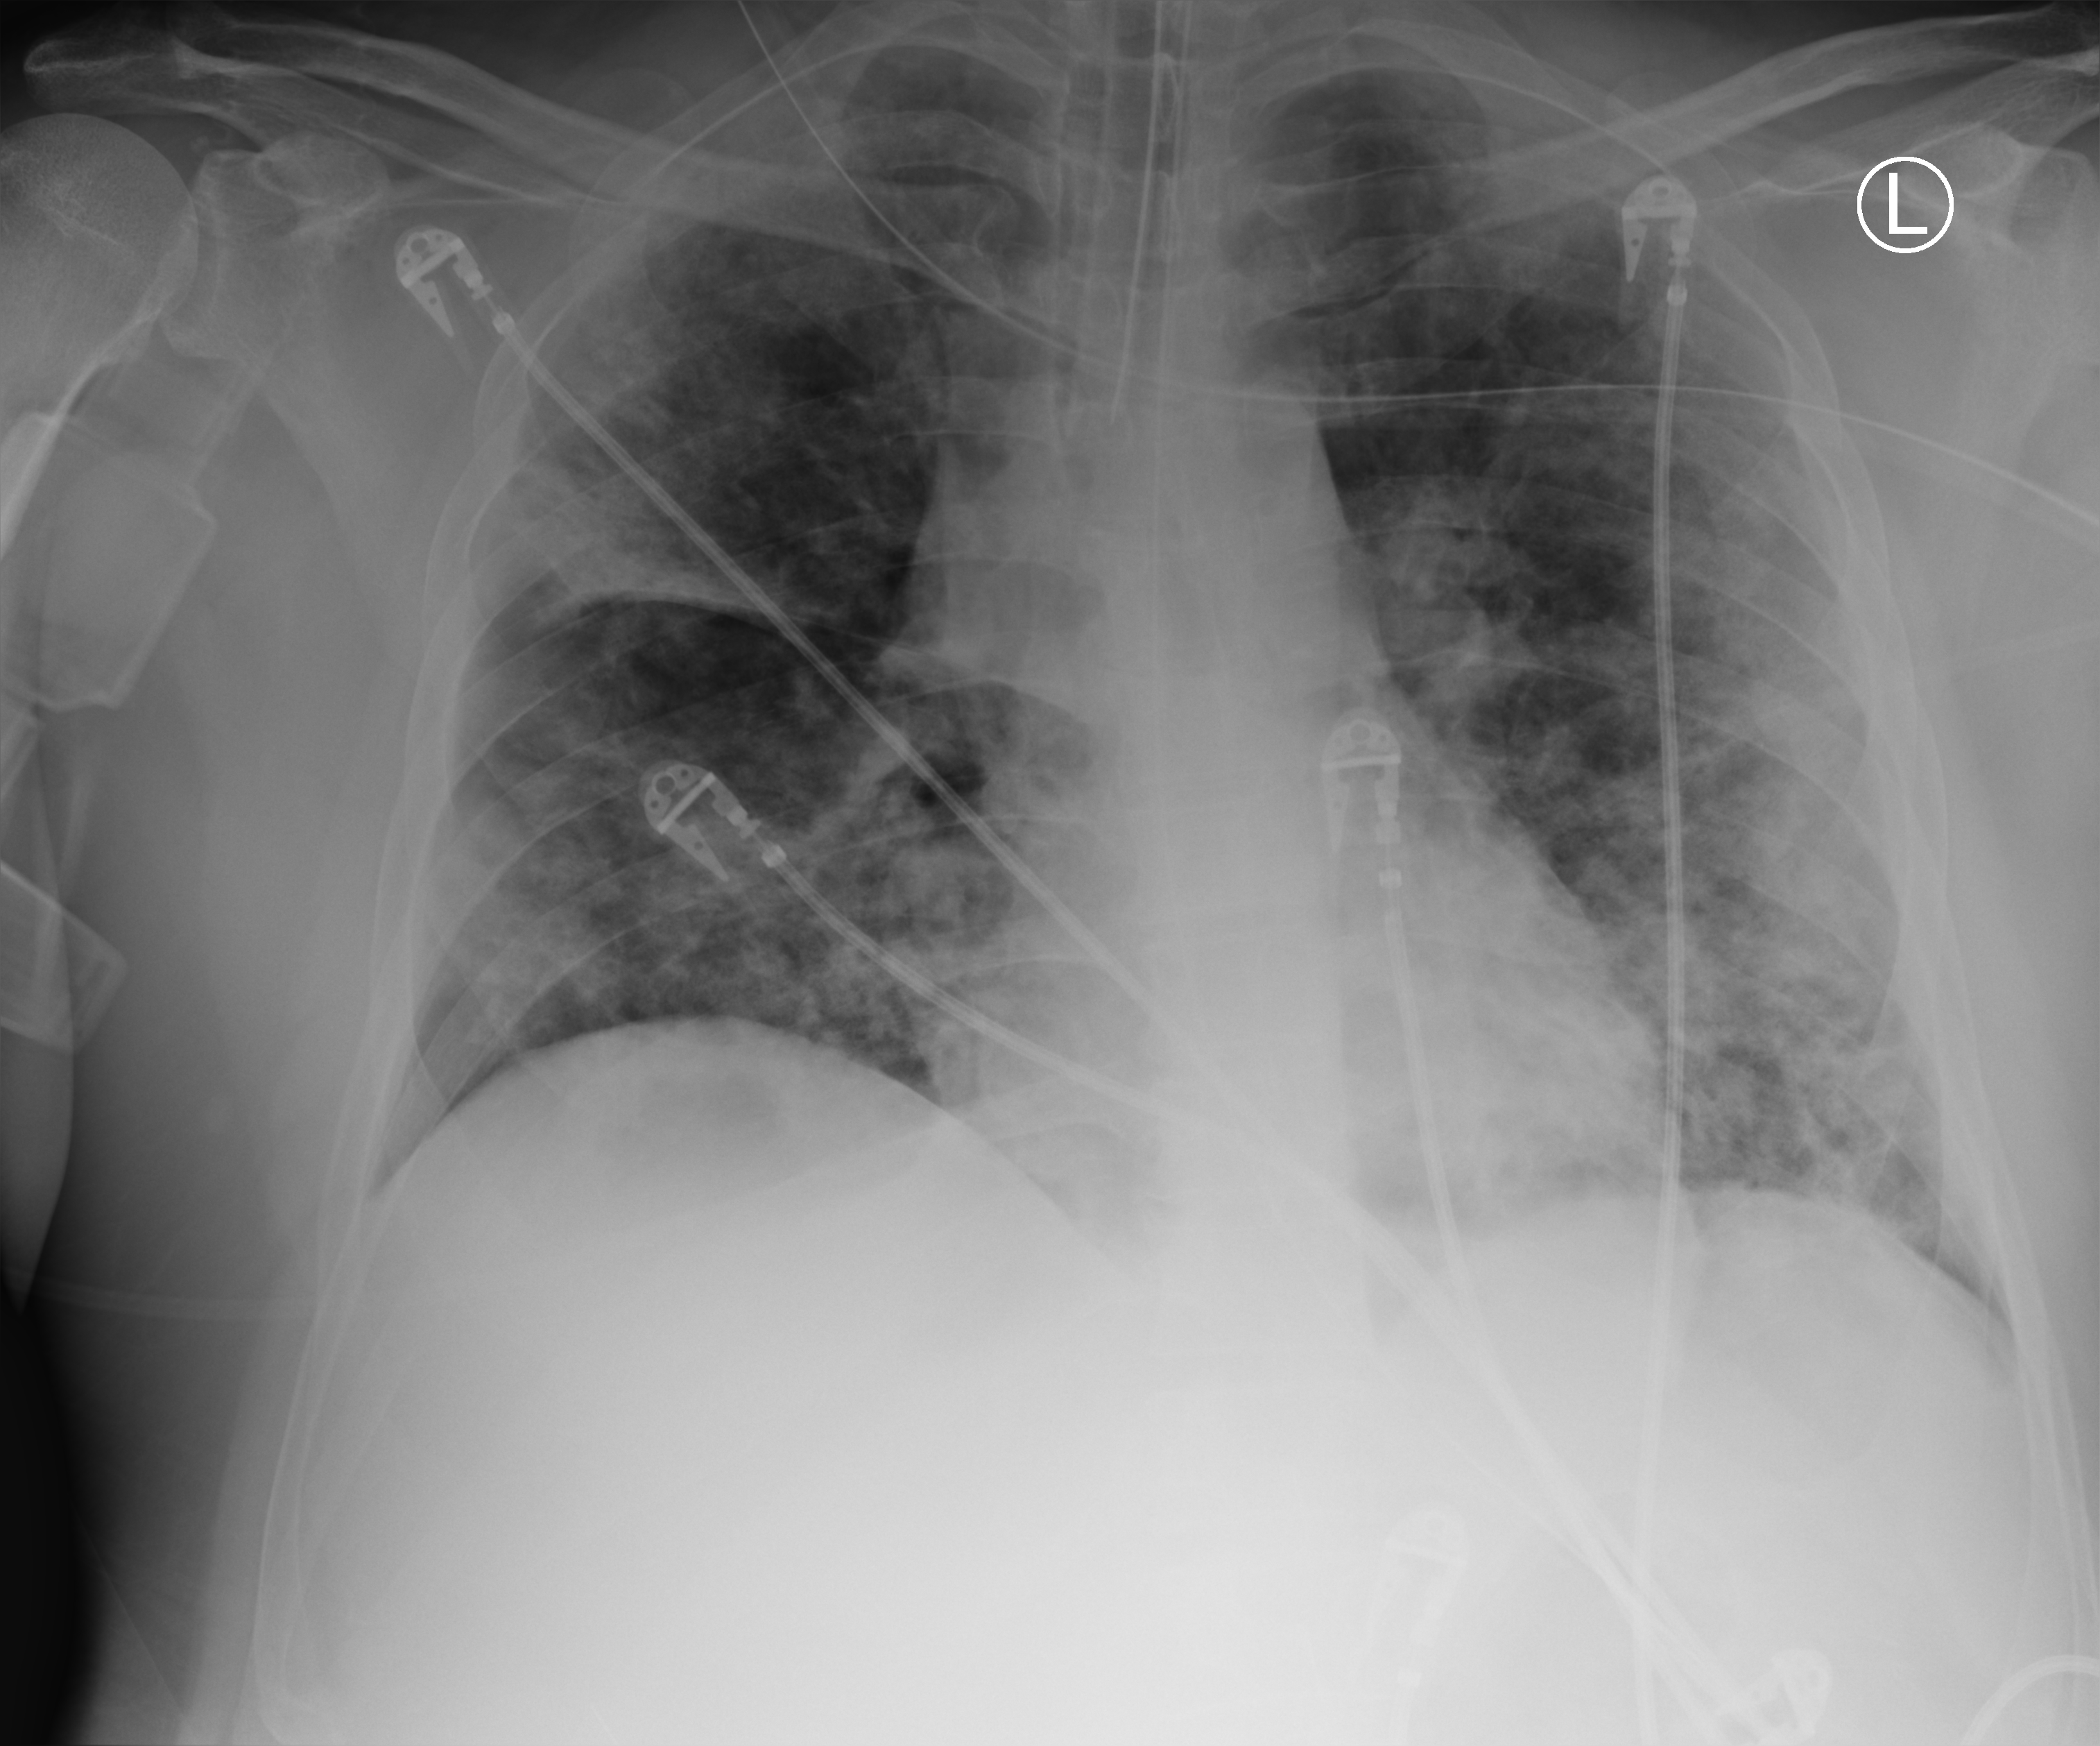
Bedside chest radiograph (computed radiography); anteroposterior (AP) projection. Adult patient hospitalised with COVID-19, age 18–59 years.
Hospital-stay facts (about this admission, not read from this image; timing relative to this image not recorded): length of hospital stay: 50 days.